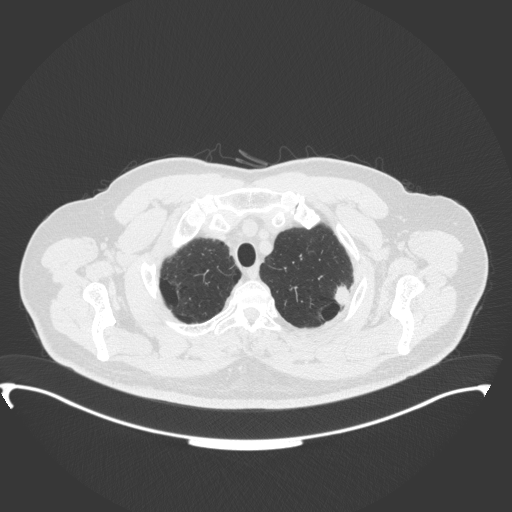
Chest CT, one axial slice. Position 321 of 350 along the scan axis. Lung window (W 1500 / L -600 HU). 1 mm slice thickness. 512 × 512 image matrix, field of view 459 × 459 mm. Patient: male, 64 years. From the clinical record (not read from this slice): clinical TNM (as recorded): T1c N1 M1.
Outlined on this slice (bounding box drawn by a radiologist):
- lung tumour (recorded histology: adenocarcinoma): bounding box [x1, y1, x2, y2] px = [330, 282, 351, 310]